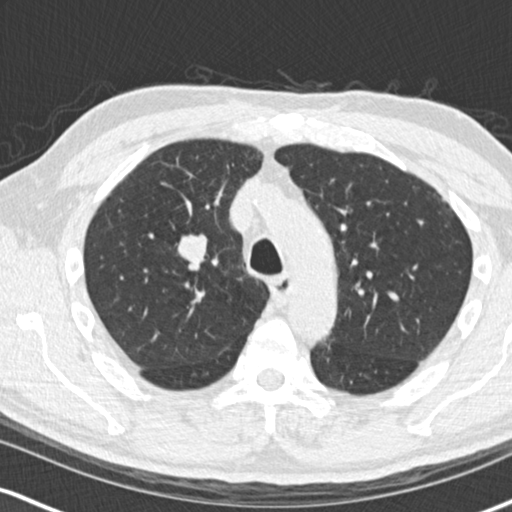
Low-dose screening chest CT, one axial slice; position 111 of 170 along the scan axis; reconstruction kernel B30f; lung window (W 1500 / L -600 HU); 2 mm slice thickness; 512 × 512 image matrix, field of view 320 × 320 mm.
Outlined on this slice (outlined manually by an expert reader):
- lesion 1 (tumor, upper lobe of right lung): bounding box [x1, y1, x2, y2] px = [178, 234, 207, 263]